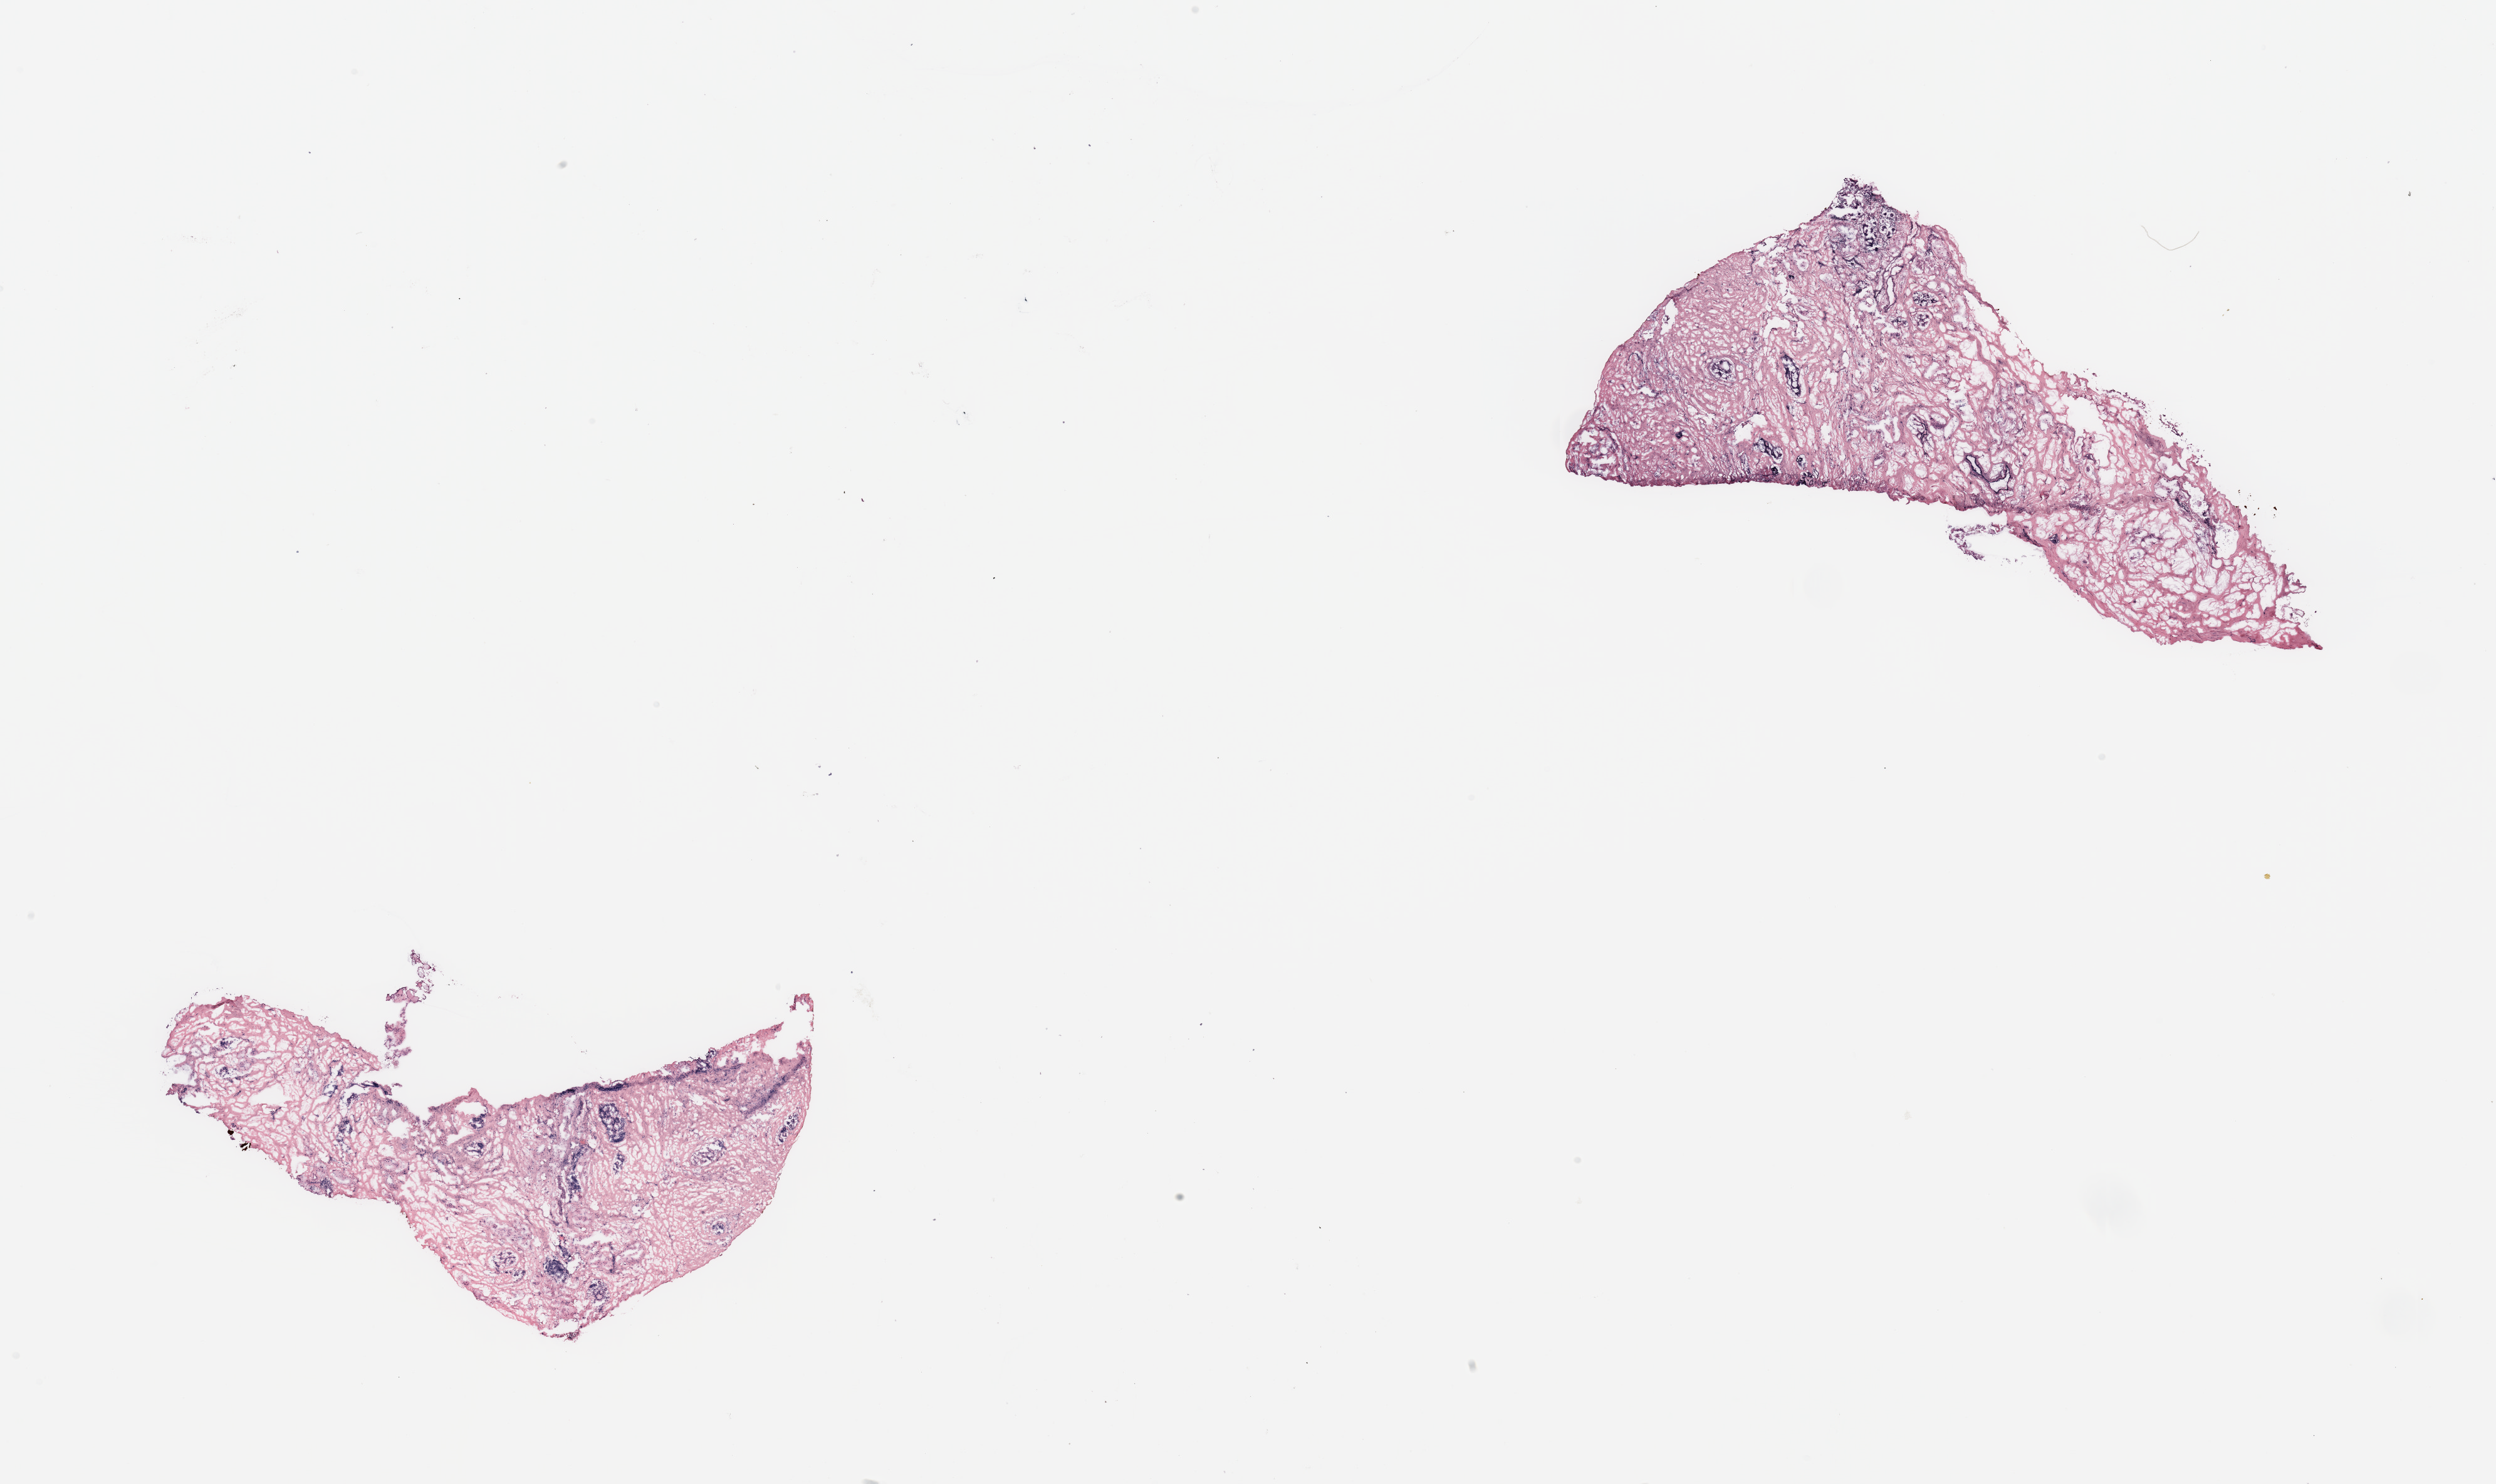
H&E whole-slide image — whole scanned area (about 31.5 x 18.7 mm, acquisition: 20x scan) shown as a low-resolution overview; breast, tissue type not recorded.
Patient diagnosis (cohort enrolment): breast cancer (breast).